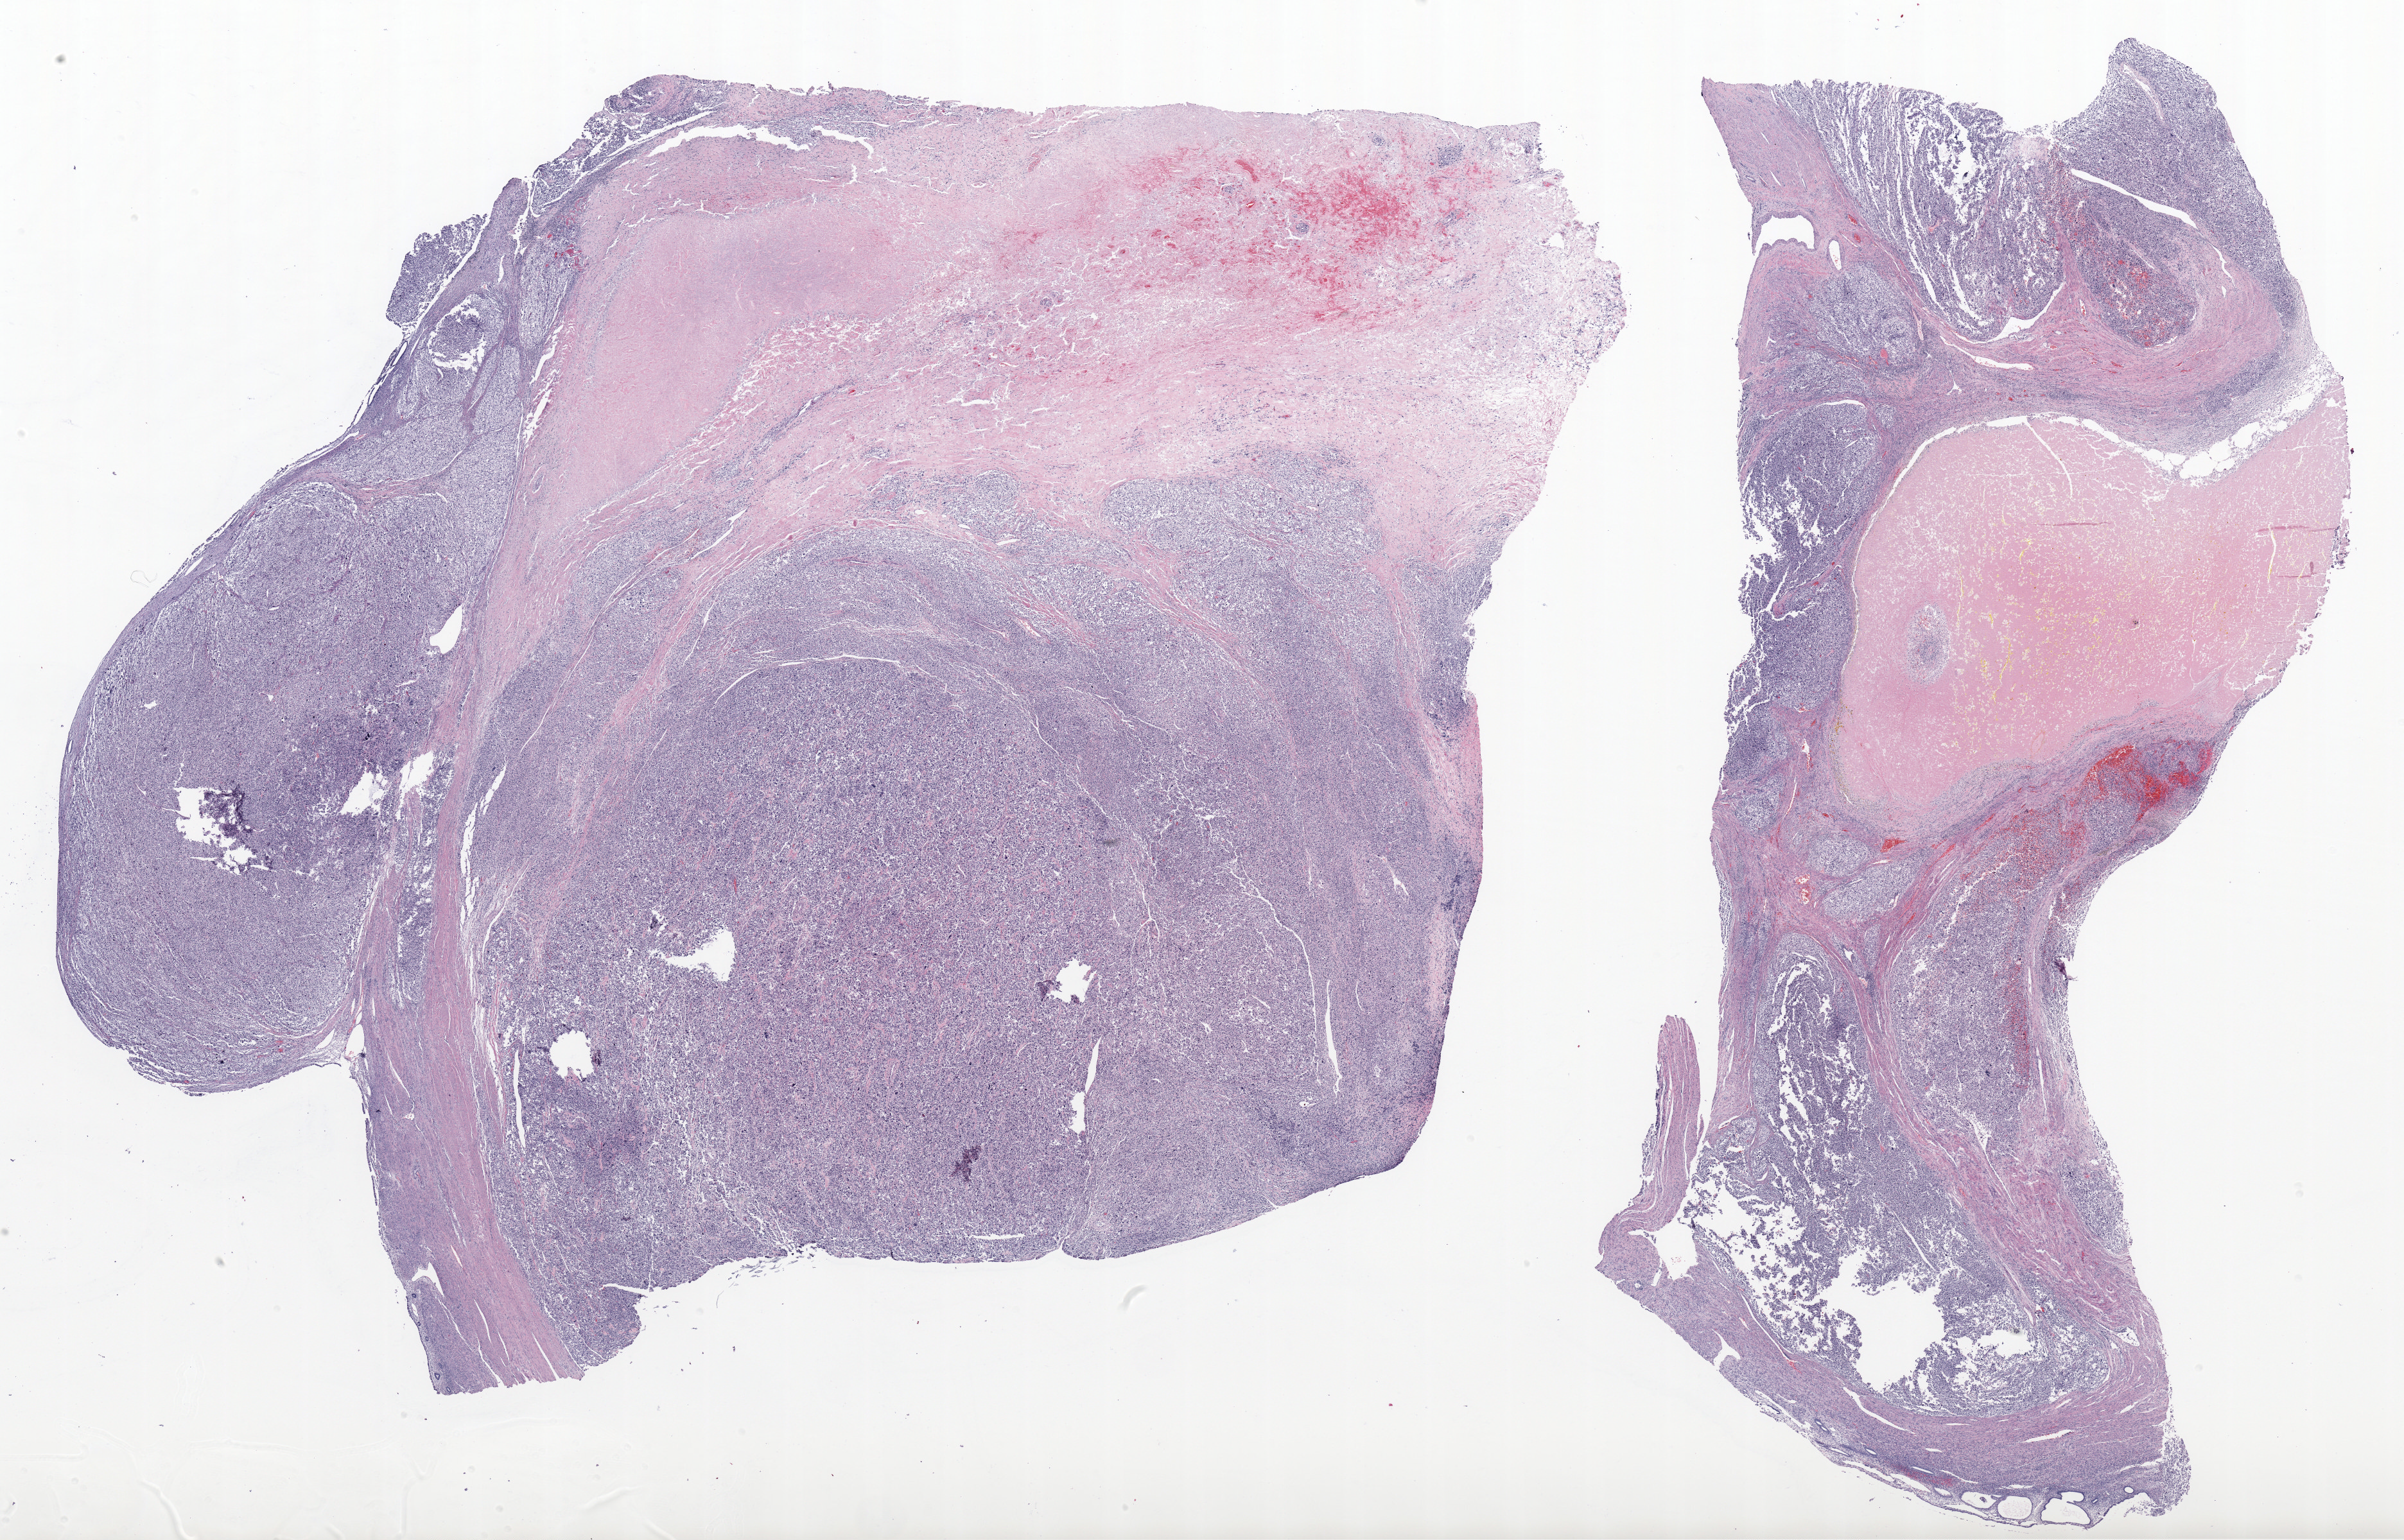
Digitized Hematoxylin and eosin (H&E) stained tissue section (whole slide) — shown as a low-resolution overview of the whole scanned area (about 29.8 x 19.1 mm, slide scanned at 20x), formalin-fixed paraffin-embedded (FFPE) diagnostic section, primary tumour sample from the uterus. Female, age 73 years at initial diagnosis.
Diagnosis: Leiomyosarcoma, NOS.